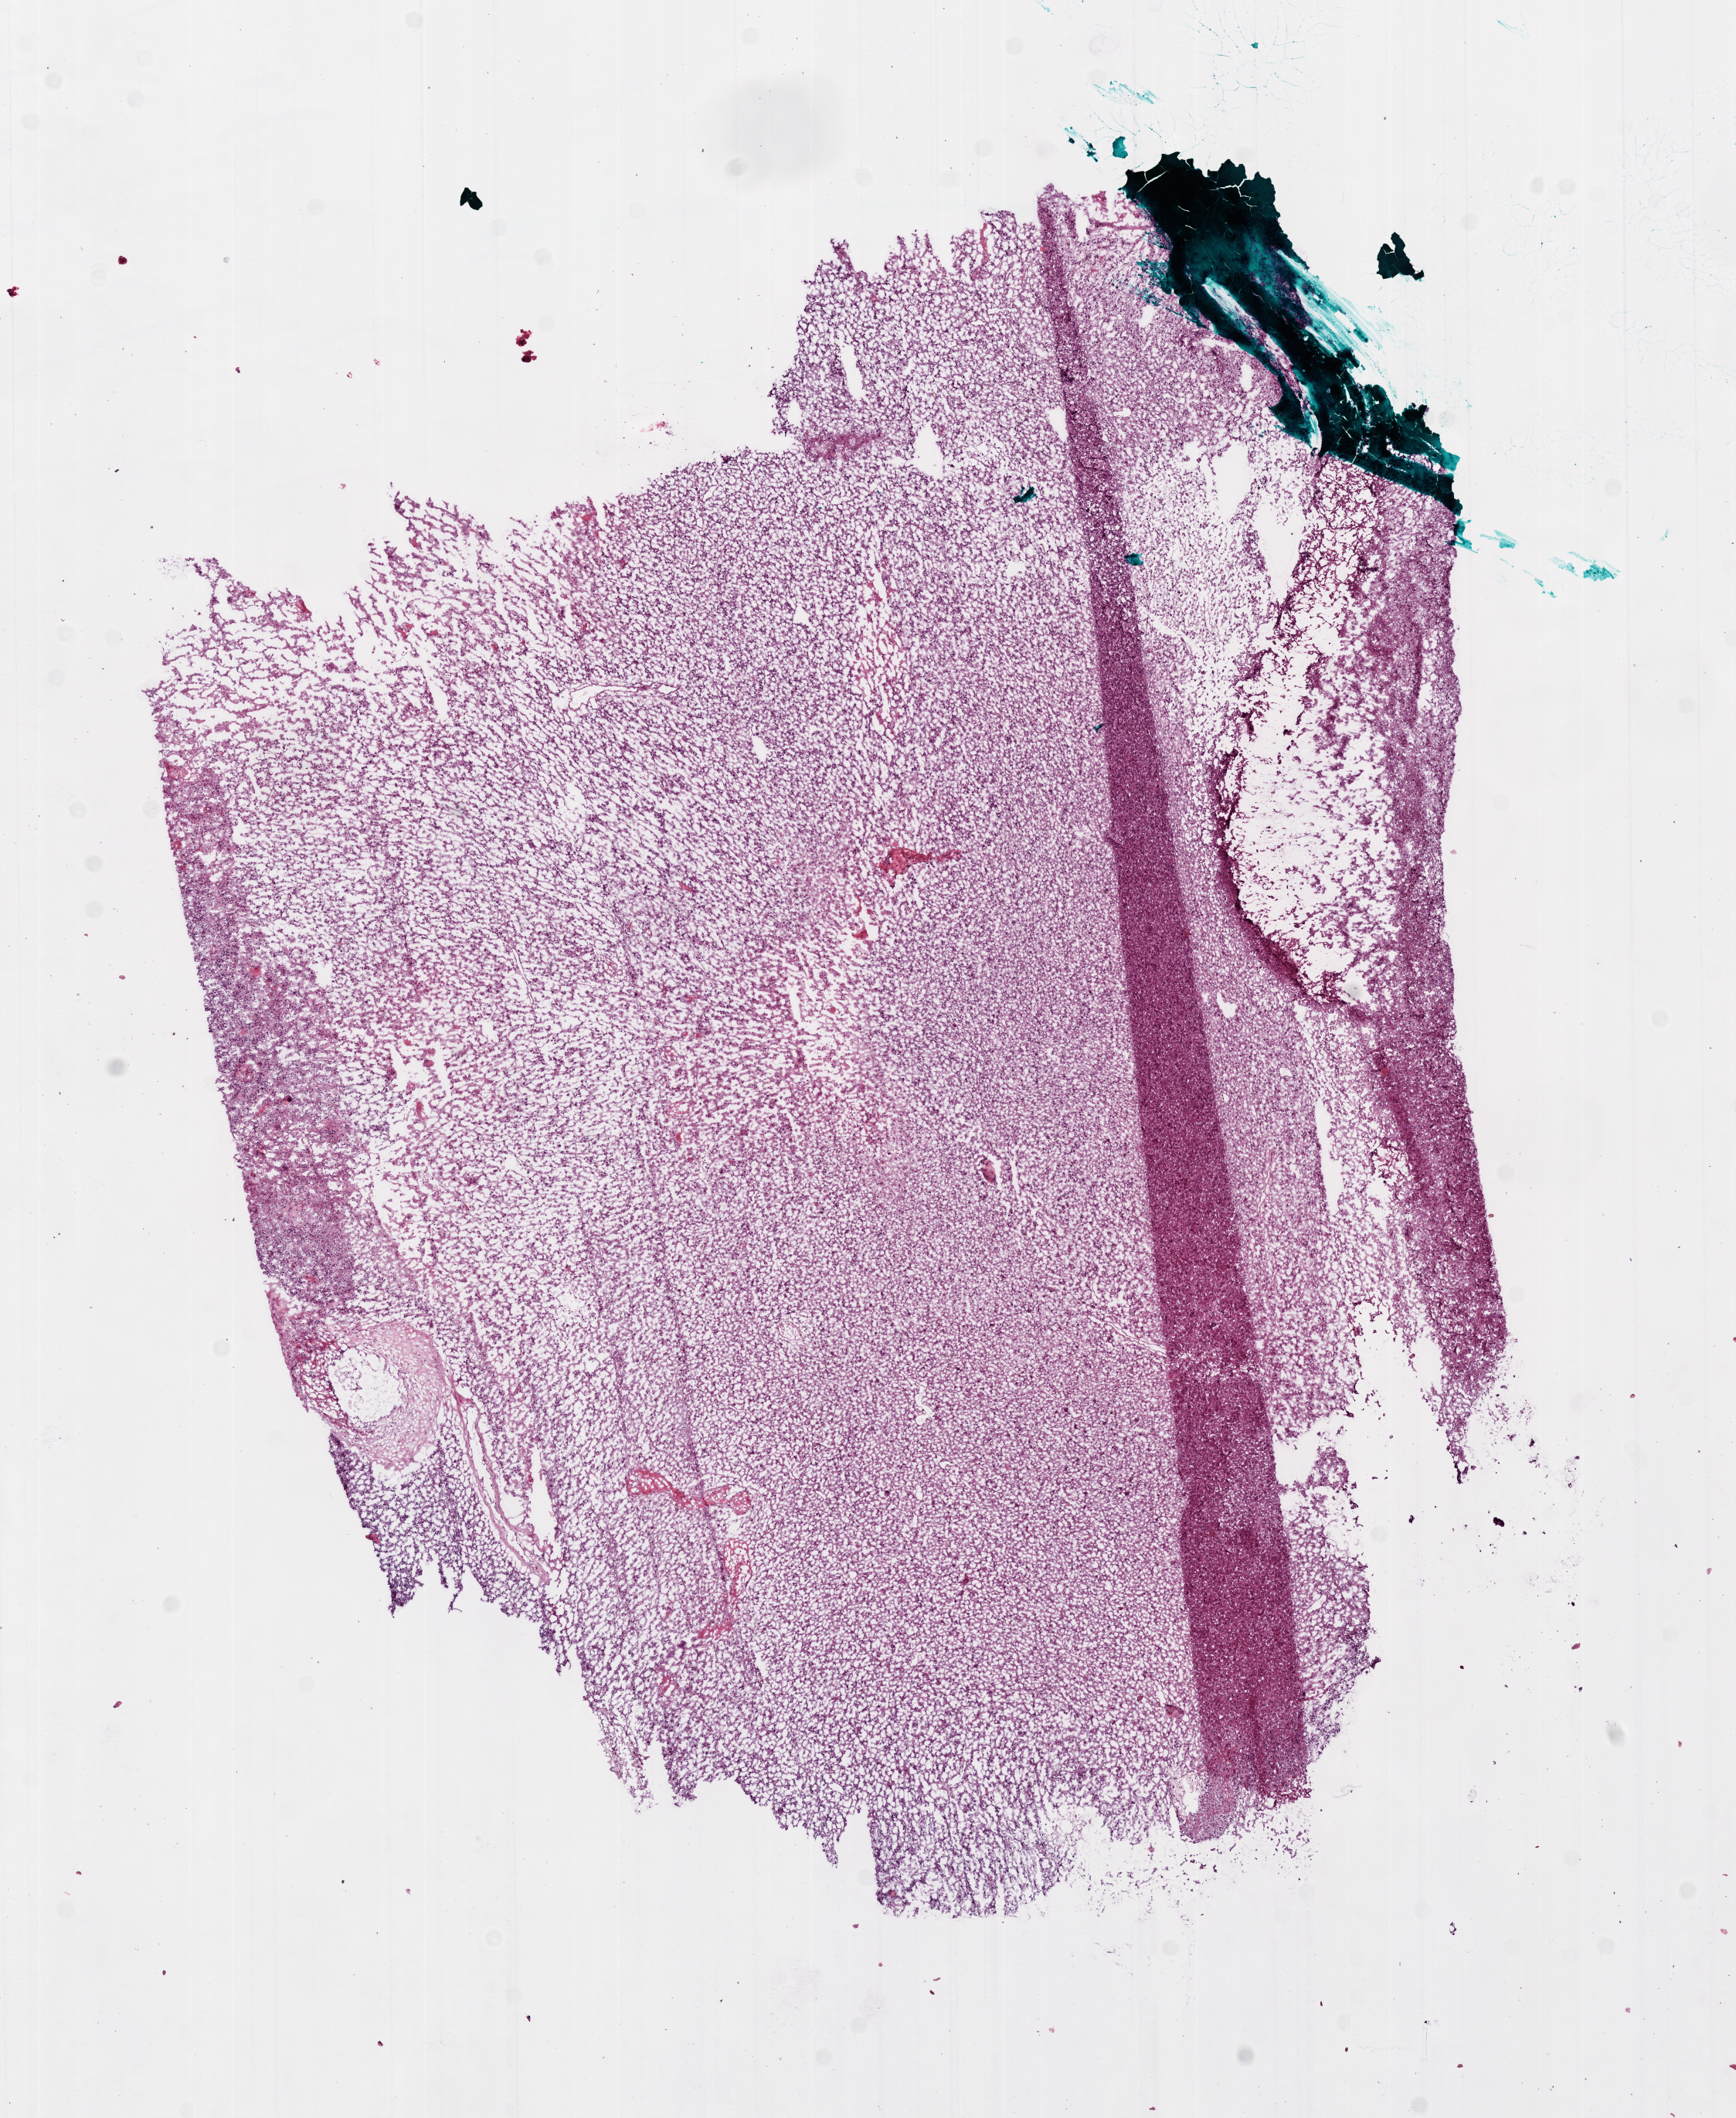
Whole-slide histology image, Hematoxylin and eosin (H&E) stained — whole scanned area (about 9.0 x 11.0 mm, acquisition: 20x scan) shown as a low-resolution overview, frozen section from the bottom of the tissue portion, brain, primary tumour sample. Male, age 64 years at initial diagnosis. Pathologist review of this section (percent, as recorded): tumour cells 25%, tumour nuclei 80%, normal cells 0%, stromal cells 65%, necrosis 10%.
Diagnosis: Glioblastoma.